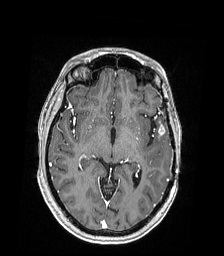
Brain MRI from a brain-tumour surgery series, one axial slice. Position 107 of 168 along the scan axis. T1-weighted post-contrast. 1 mm slice thickness. 224 × 256 image matrix, field of view 224 × 256 mm. Case-level facts recorded for this patient, not image findings: histopathology: Astrocytoma; WHO grade: 4; IDH mutation: yes; tumour location: Left Temporal.
Outlined on this slice (outlined manually by an expert reader):
- tumour: box from (x=152, y=122) to (x=166, y=148) px